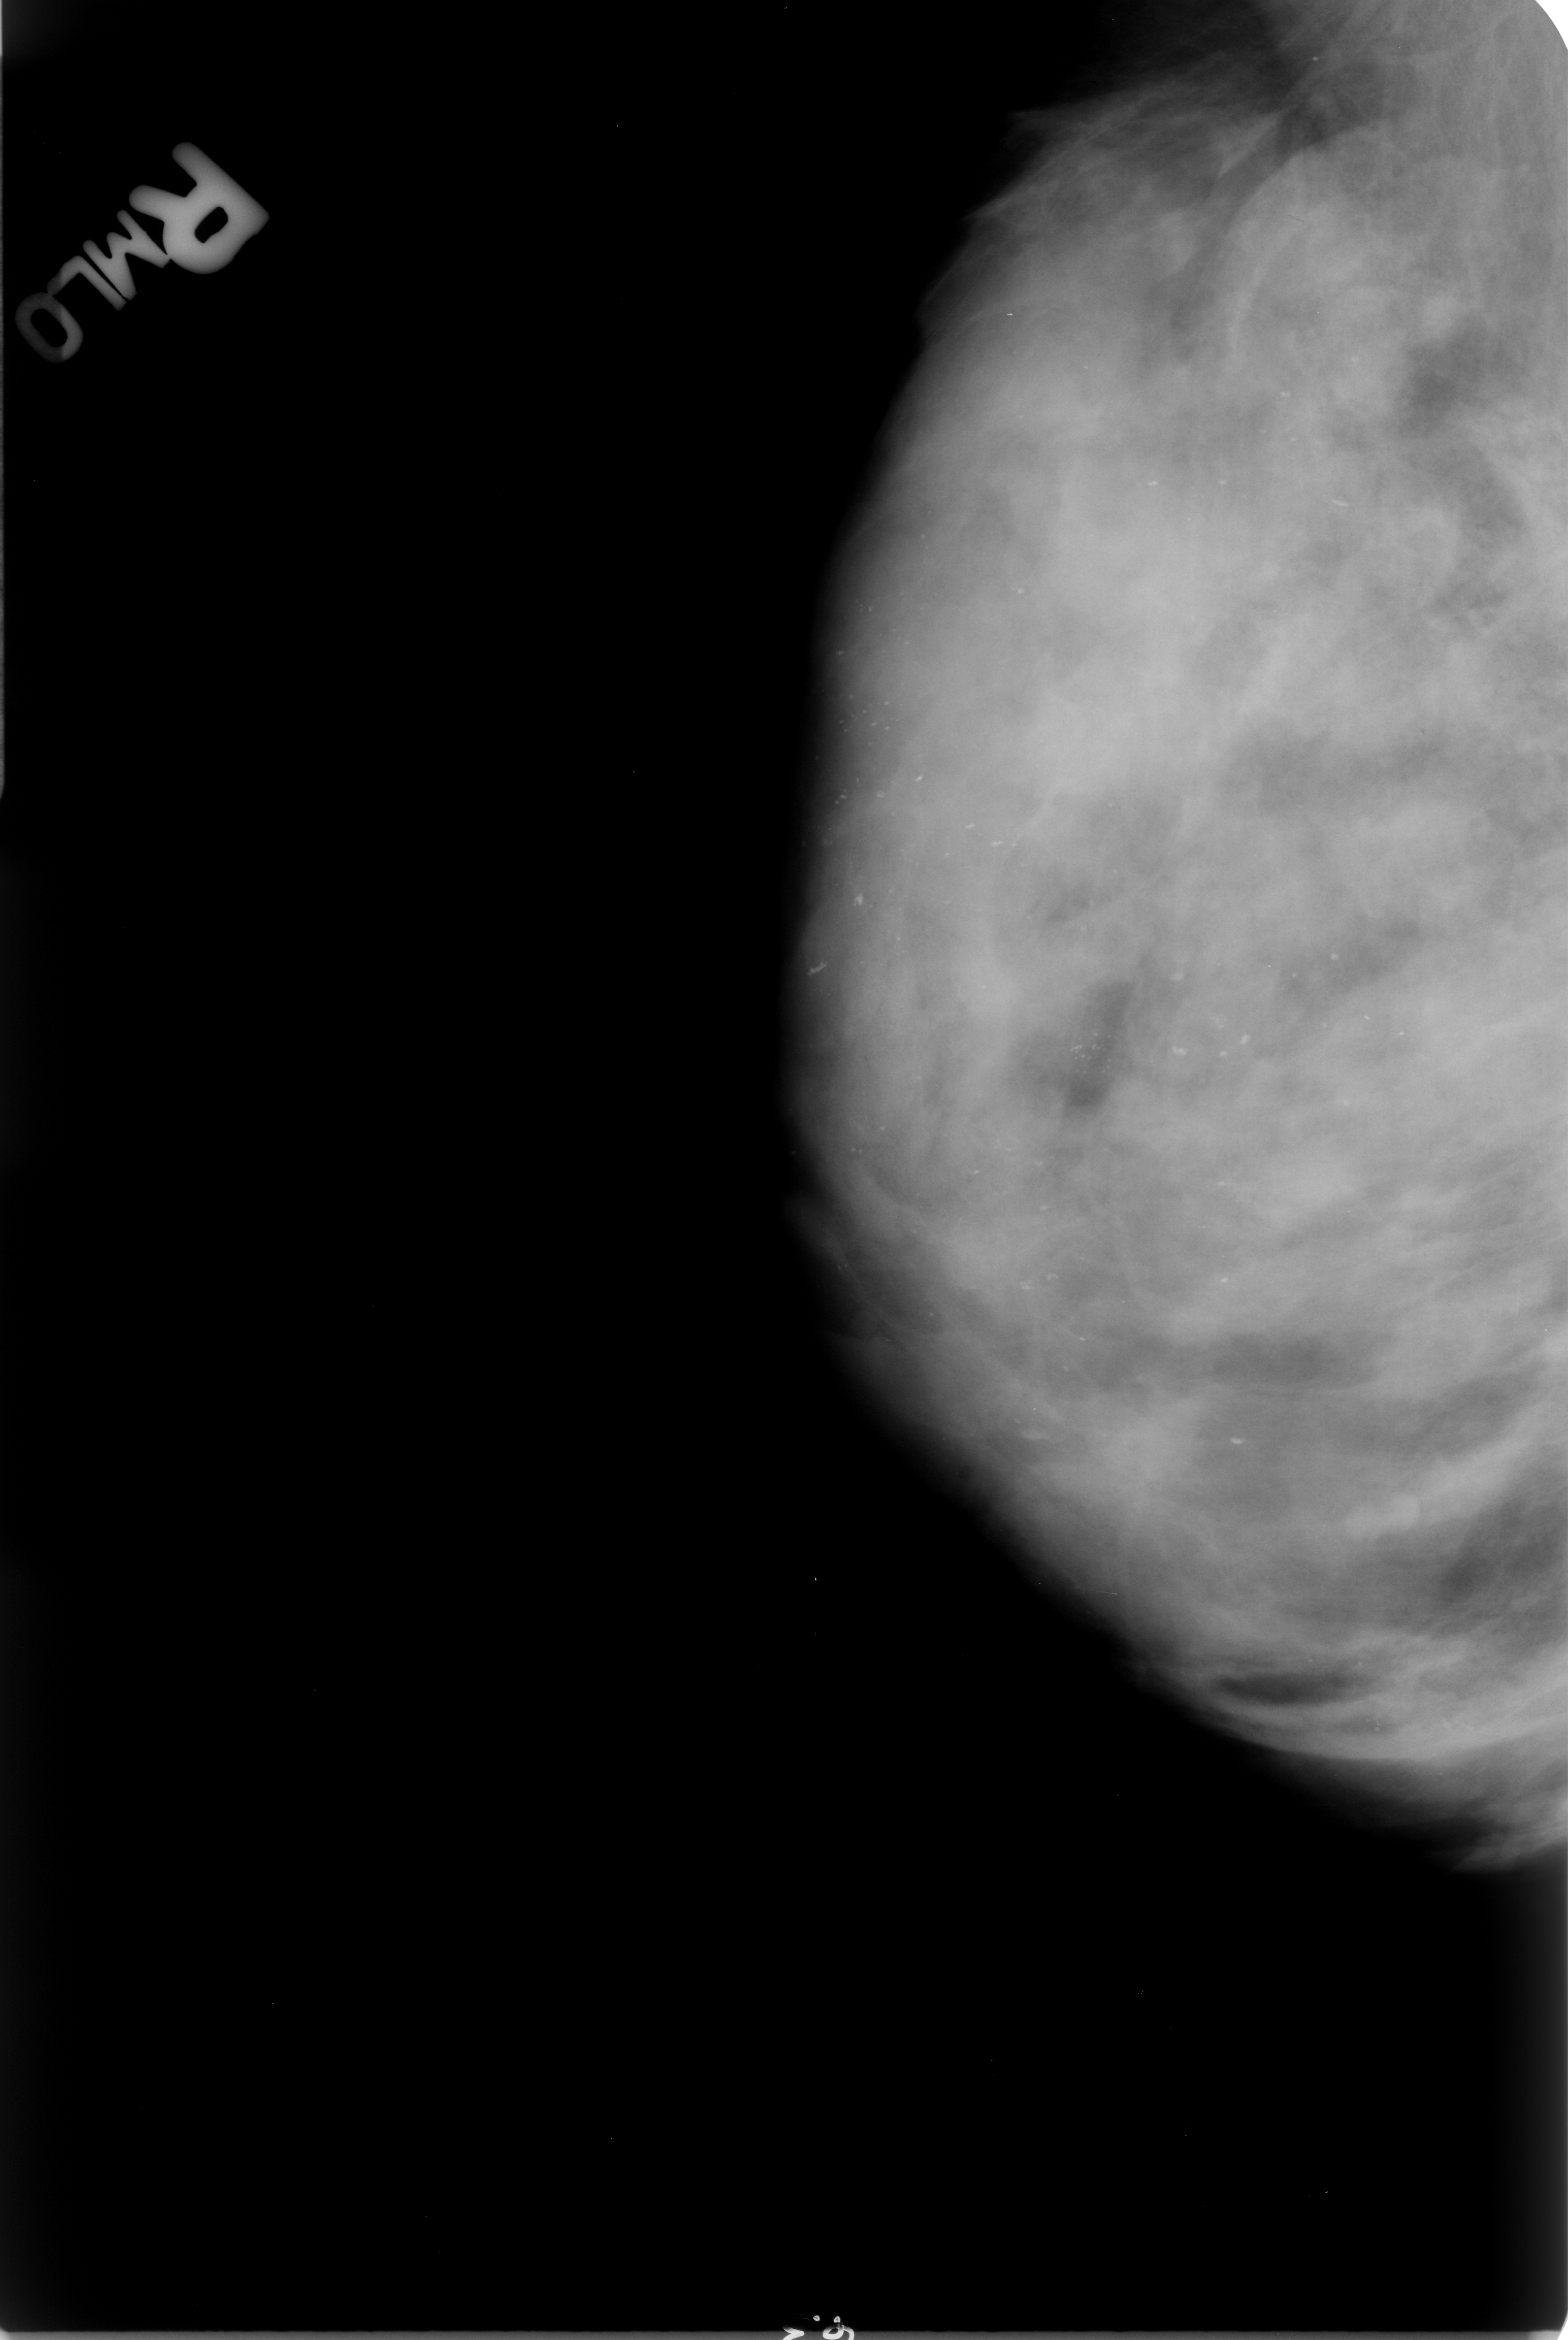
Scanned film-screen mammogram; right breast; MLO view; BI-RADS breast density category 4 (scale 1–4); 1568 × 2340 image matrix.
Expert-marked regions of interest on this film, with their recorded descriptors:
- calcifications, morphology punctate / pleomorphic, distribution clustered; BI-RADS assessment category 4; pathology (as recorded): benign: bounding box (x1, y1, x2, y2) in pixels: (1003, 970, 1130, 1114)